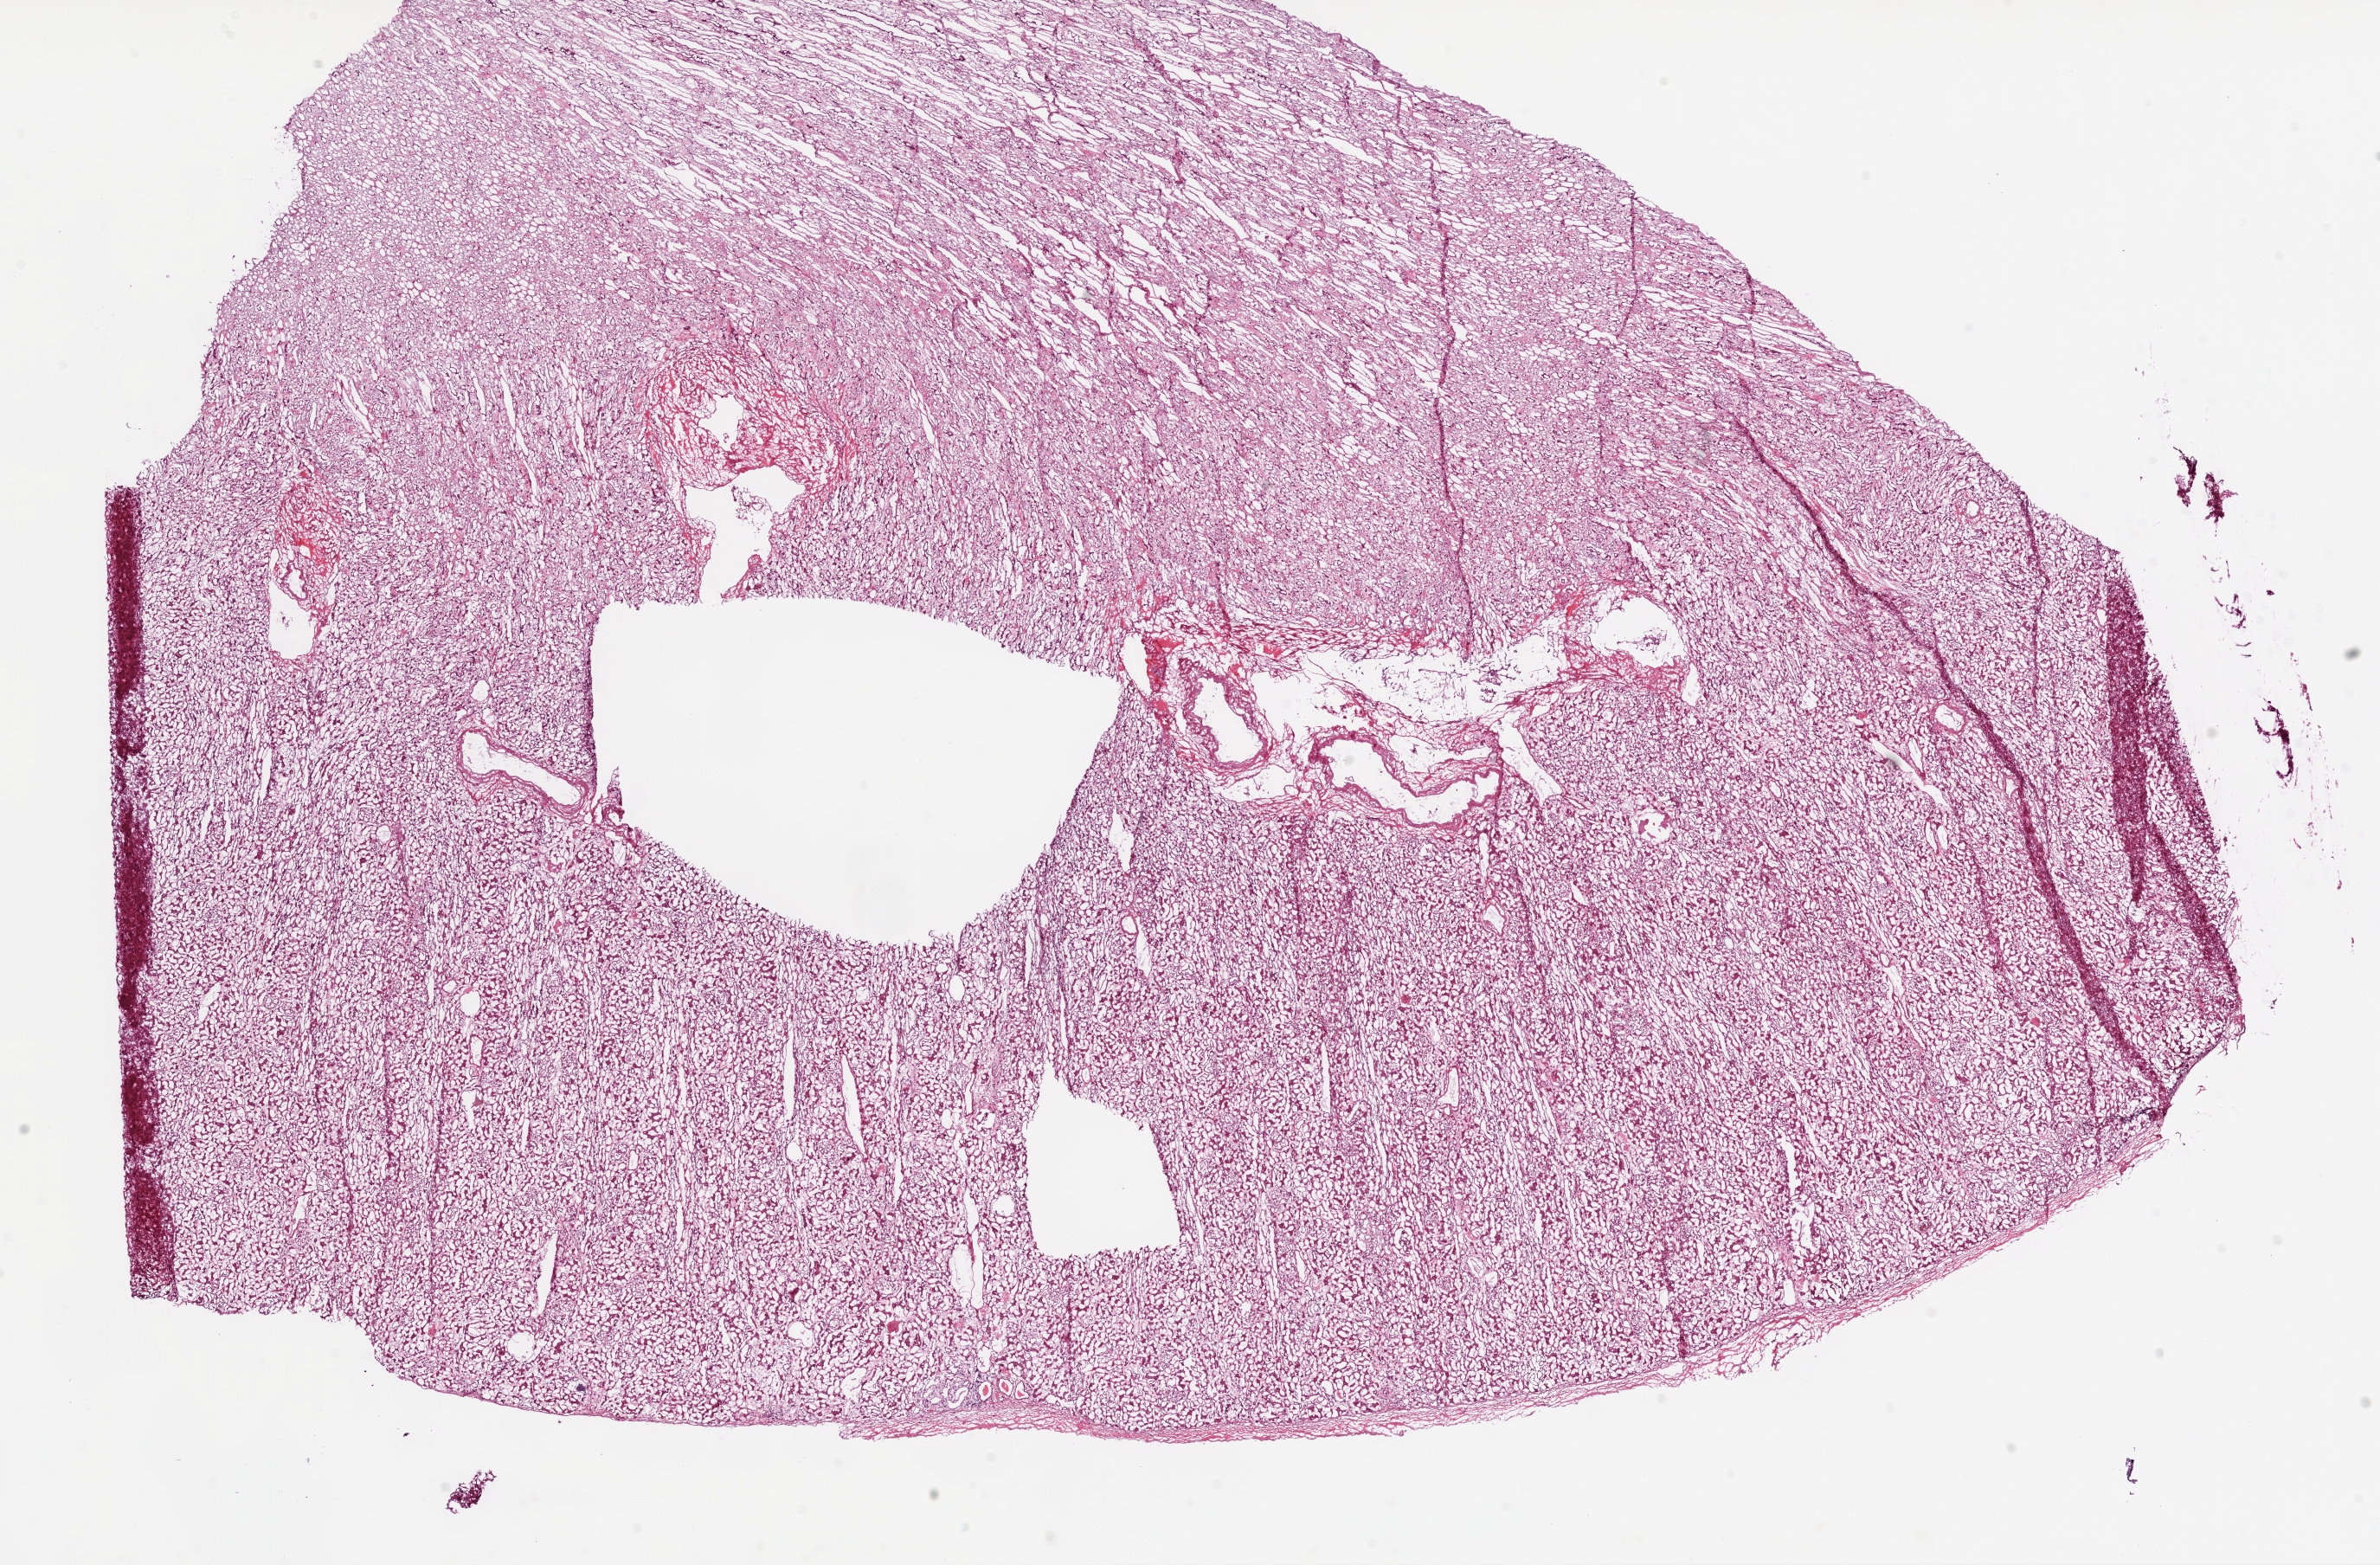
Digitized H&E tissue section (whole slide), shown as a low-resolution overview of the whole scanned area (about 22.1 x 14.5 mm). Frozen section from the bottom of the tissue portion. Solid tissue normal (non-tumour tissue) sample from the kidney. Female patient; age at initial diagnosis 65 years.
- this section: solid tissue normal sample (biorepository sample class)
- patient diagnosis: Clear cell adenocarcinoma, NOS